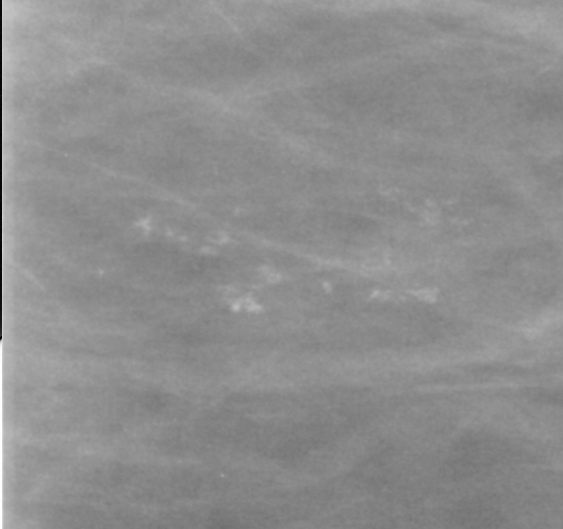
Region of interest cut from a scanned film mammogram (one marked finding); left breast; CC view; BI-RADS breast density category 1 (scale 1–4).
Calcifications, morphology pleomorphic, distribution segmental; BI-RADS assessment category 0 (incomplete: needs additional imaging); pathology (as recorded): benign.